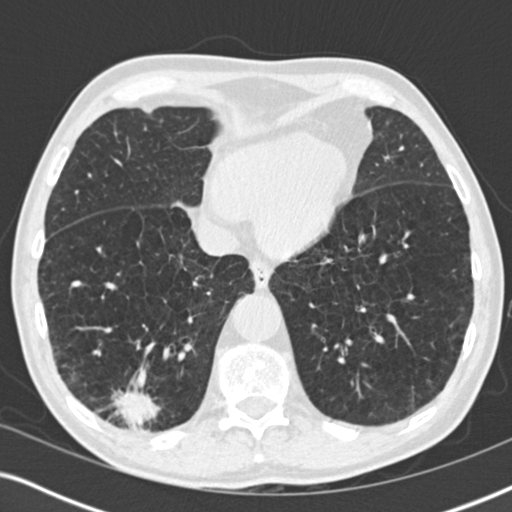
Axial slice from a low-dose chest CT screening exam, first (baseline) screen, lung window (W 1500 / L -600 HU), standard (soft-tissue) reconstruction kernel (B30f), slice 136 of 196 in the series. Male participant, aged 64 years at enrolment. Former smoker at enrolment.
Expert-annotated lung lesion, box from (x=86, y=370) to (x=179, y=447) px. The screening reader recorded 3 non-calcified nodules or masses ≥4 mm on this exam; which of them this box marks is not recorded. Participant outcome: lung cancer diagnosed 27 days after this screen — squamous cell carcinoma, NOS, right lower lobe, moderately differentiated (G2), stage IV (AJCC 6th edition), 40 mm at pathology.